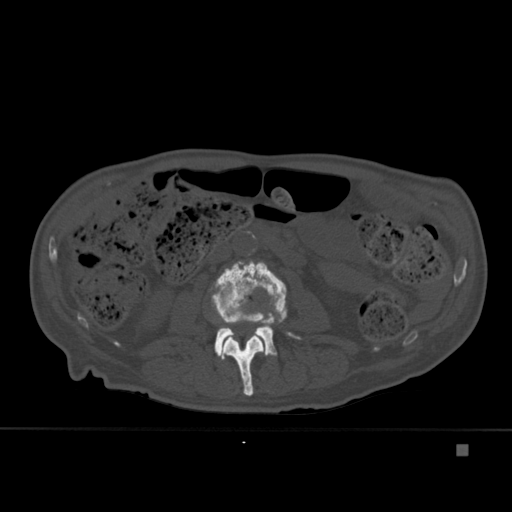
CT including the spine, one axial slice. Position 151 of 451 along the scan axis. Bone window (W 1800 / L 400 HU). 1.5 mm slice thickness. 512 × 512 image matrix, field of view 378 × 378 mm. Patient: male, 75 years. From the clinical record (not read from this slice): primary cancer: prostate.
Annotated regions visible in this slice (semi-automatically segmented with operator editing):
- L2 vertebra: bounding box <221,311,265,397> (left, top, right, bottom; pixels)
- L3 vertebra: <210,260,301,359>